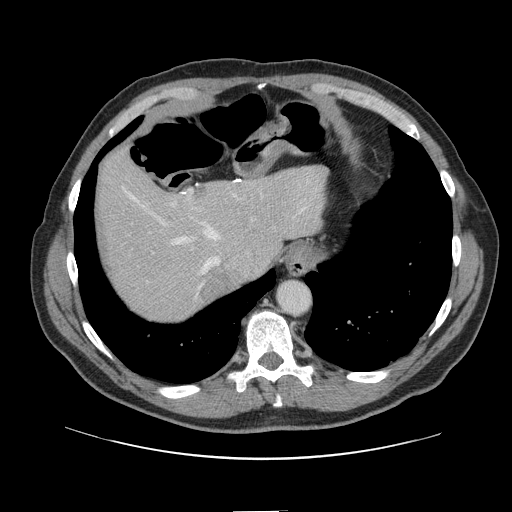
Contrast-enhanced abdominal CT, one axial slice. Slice 117 of 161 in the series (ordered by position). 120 kVp. Intravenous contrast given. Soft-tissue window (W 400 / L 40 HU). 2.5 mm slice thickness. 512 × 512 image matrix, field of view 412 × 412 mm. Male patient, age 66 years. Case-level facts recorded for this patient, not image findings: diagnosis: colorectal cancer liver metastases, imaged before liver resection; multiple liver metastases: no; largest metastasis: 3.5 cm; disease in both lobes: no.
Annotated regions visible in this slice (outlined manually by an expert reader):
- hepatic veins: box from (x=122, y=186) to (x=308, y=298) px
- liver: (x=99, y=152)–(x=324, y=318)
- planned liver remnant (the part of the liver to remain after resection): (x=99, y=154)–(x=324, y=302)
- portal vein (with intrahepatic branches): (x=171, y=190)–(x=192, y=206)
- liver metastasis: (x=203, y=266)–(x=232, y=300)